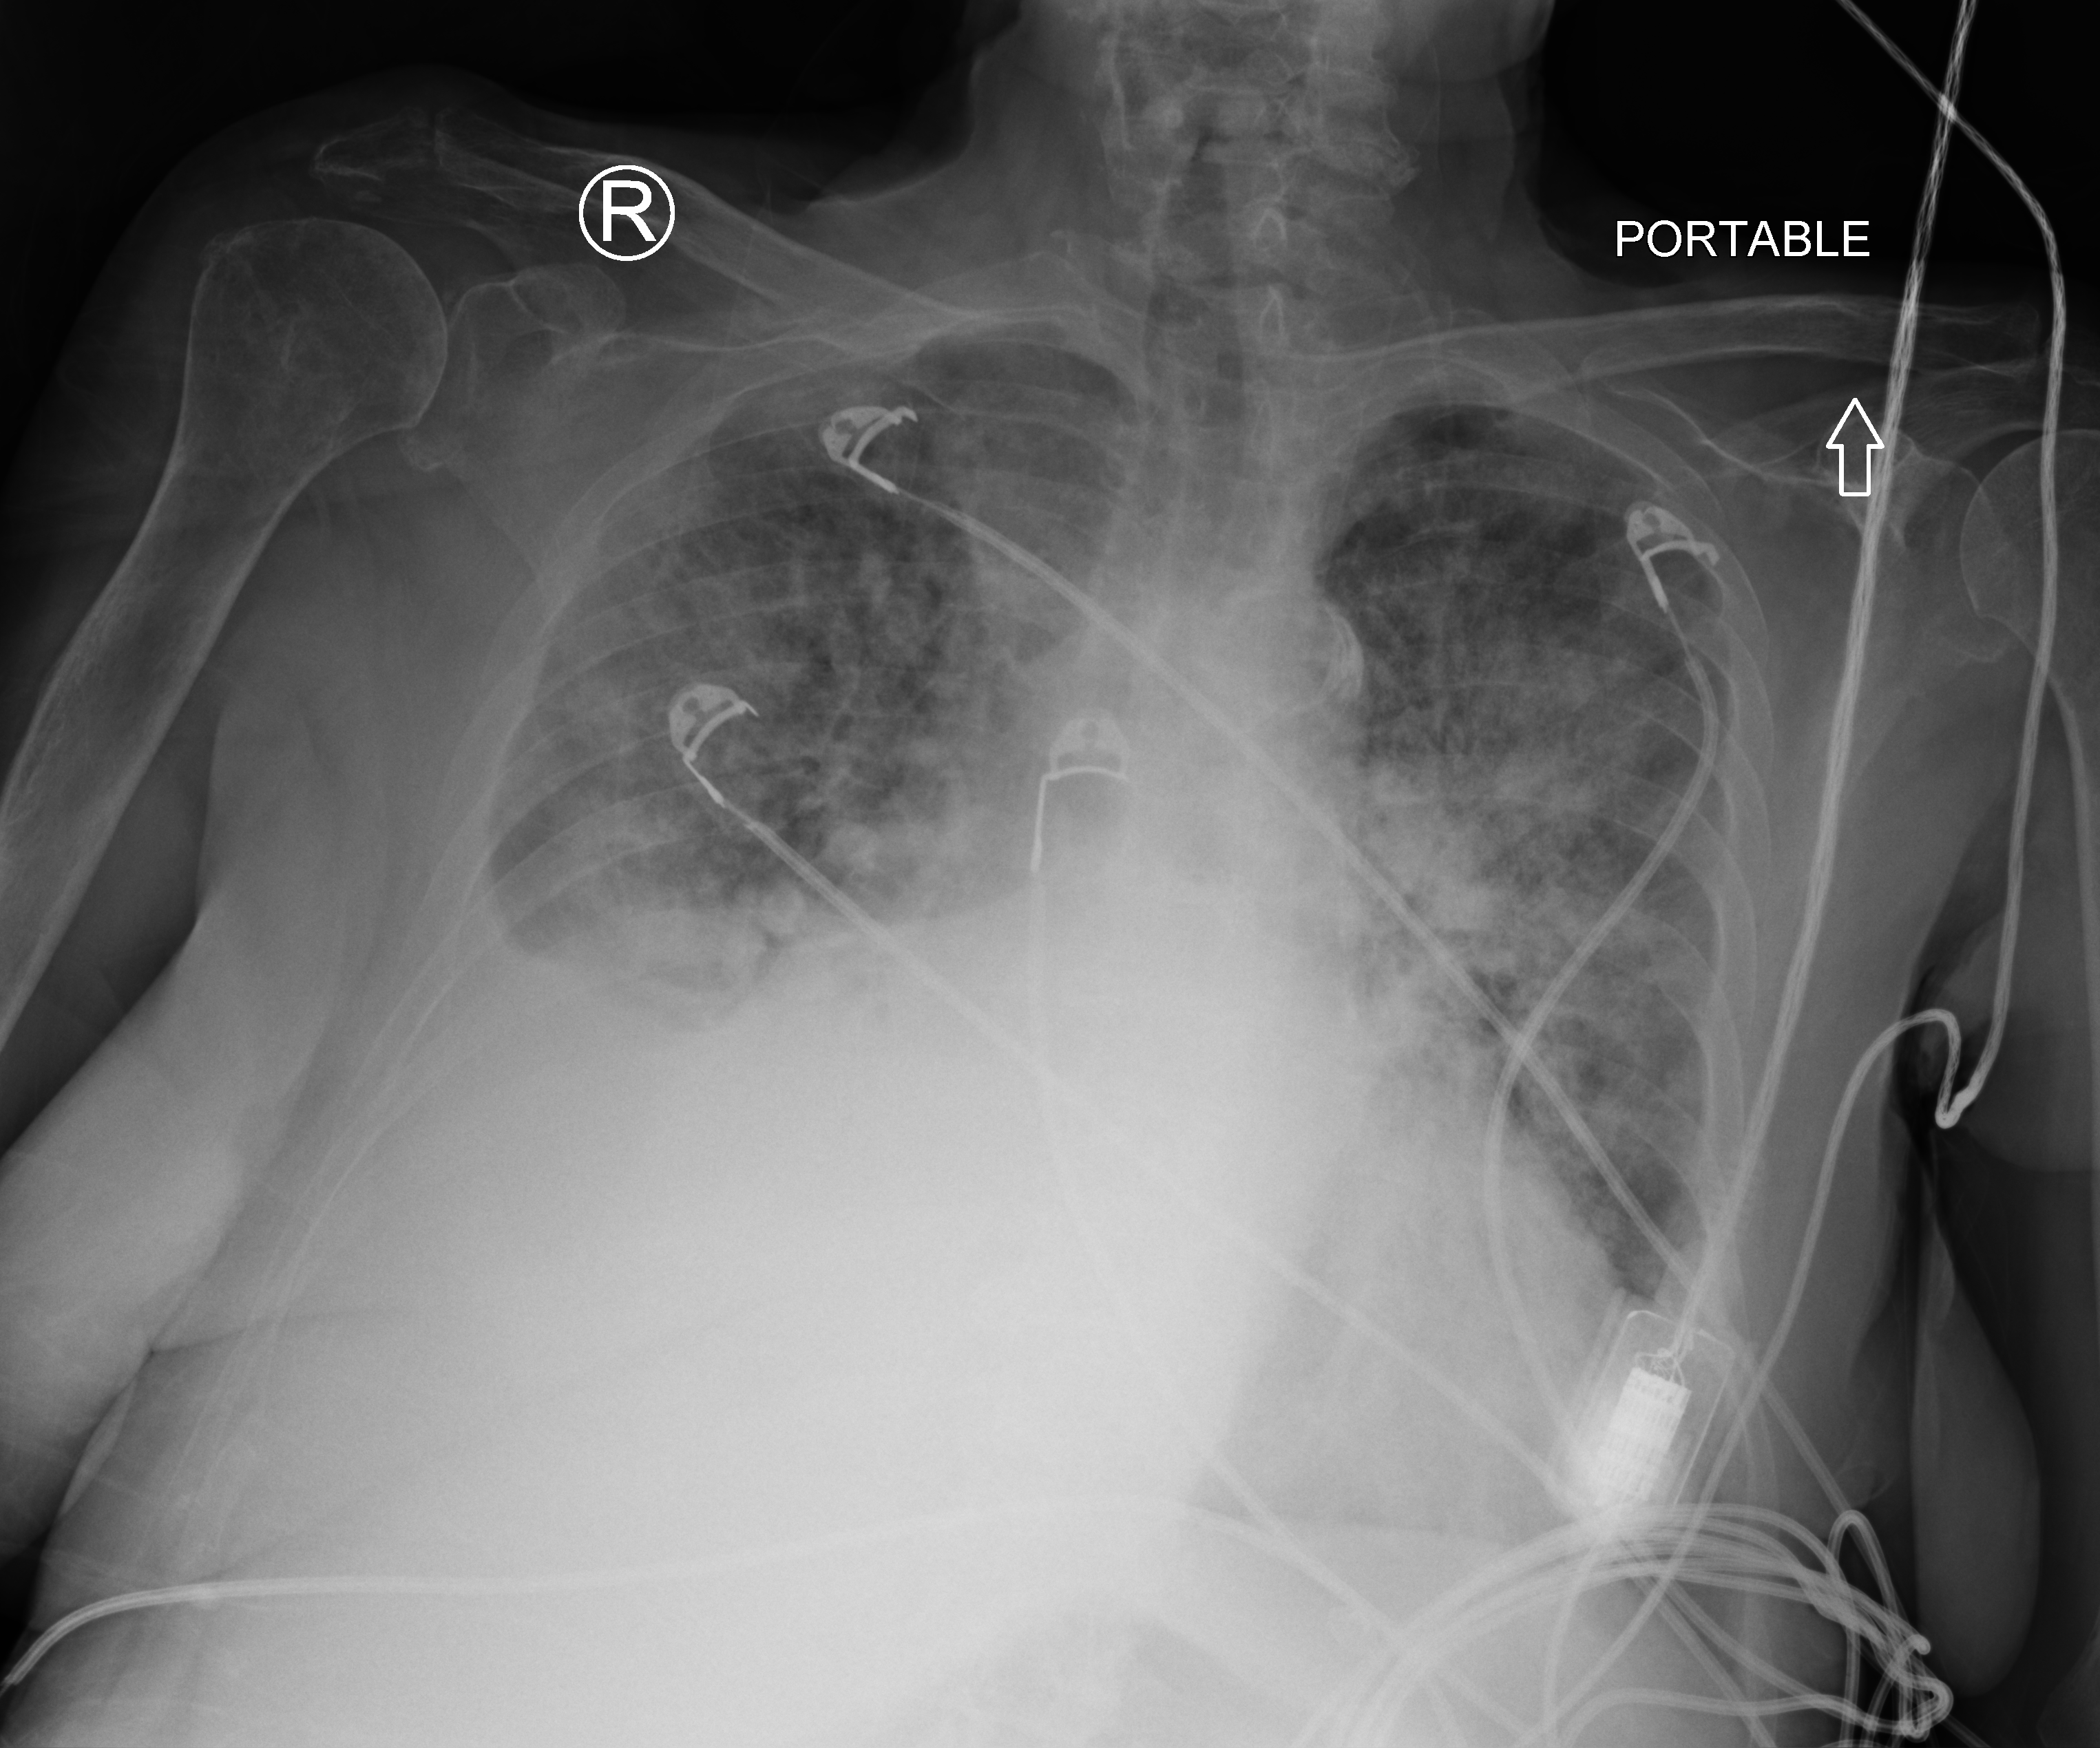
Chest X-ray (portable); anteroposterior (AP) projection. Patient hospitalised with COVID-19; female, aged 75–90 years.
Hospital-stay facts (about this admission, not read from this image; timing relative to this image not recorded):
- mechanically ventilated during this hospital stay: no
- COPD (admission record): yes
- admitted to intensive care during this hospital stay: yes